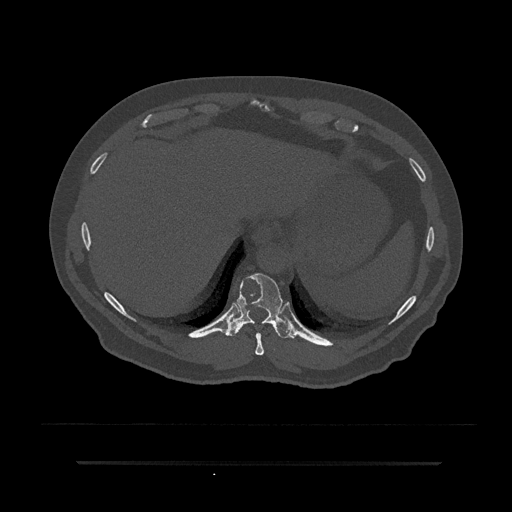
CT including the spine, one axial slice. Slice 342 of 797 in the series (ordered by position). 120 kVp. Bone window (W 1800 / L 400 HU). 0.5 mm slice thickness. 512 × 512 image matrix, field of view 464 × 464 mm. Patient: male, 59 years. From the clinical record (not read from this slice): primary cancer: bile ducts; vertebrae with lytic lesions (as recorded): T10.
Structures marked on this image (semi-automatically segmented with operator editing):
- T10 vertebra: bounding box [x1, y1, x2, y2] px = [226, 273, 295, 339]
- T9 vertebra: [255, 333, 264, 356]